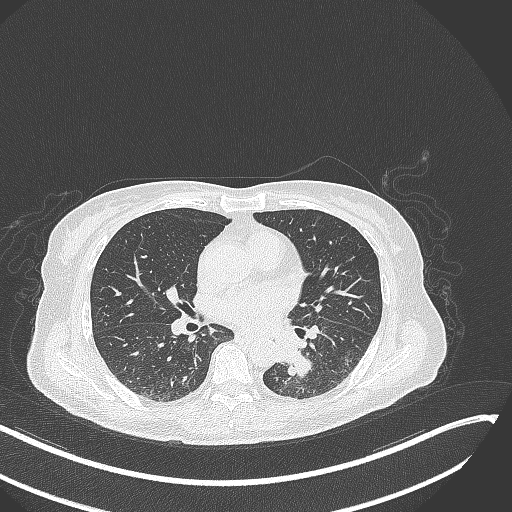
Chest CT, one axial slice; slice 132 of 342 in the series (ordered by position); lung window (W 1500 / L -600 HU); 1 mm slice thickness; 512 × 512 image matrix, field of view 400 × 400 mm. Patient: female, 64 years. Case-level facts recorded for this patient, not image findings: clinical TNM (as recorded): T3 N1 M1; histopathological grade: G3.
Structures marked on this image (bounding box drawn by a radiologist):
- lung tumour (recorded histology: small cell carcinoma): bounding box [x1, y1, x2, y2] px = [276, 335, 319, 386]